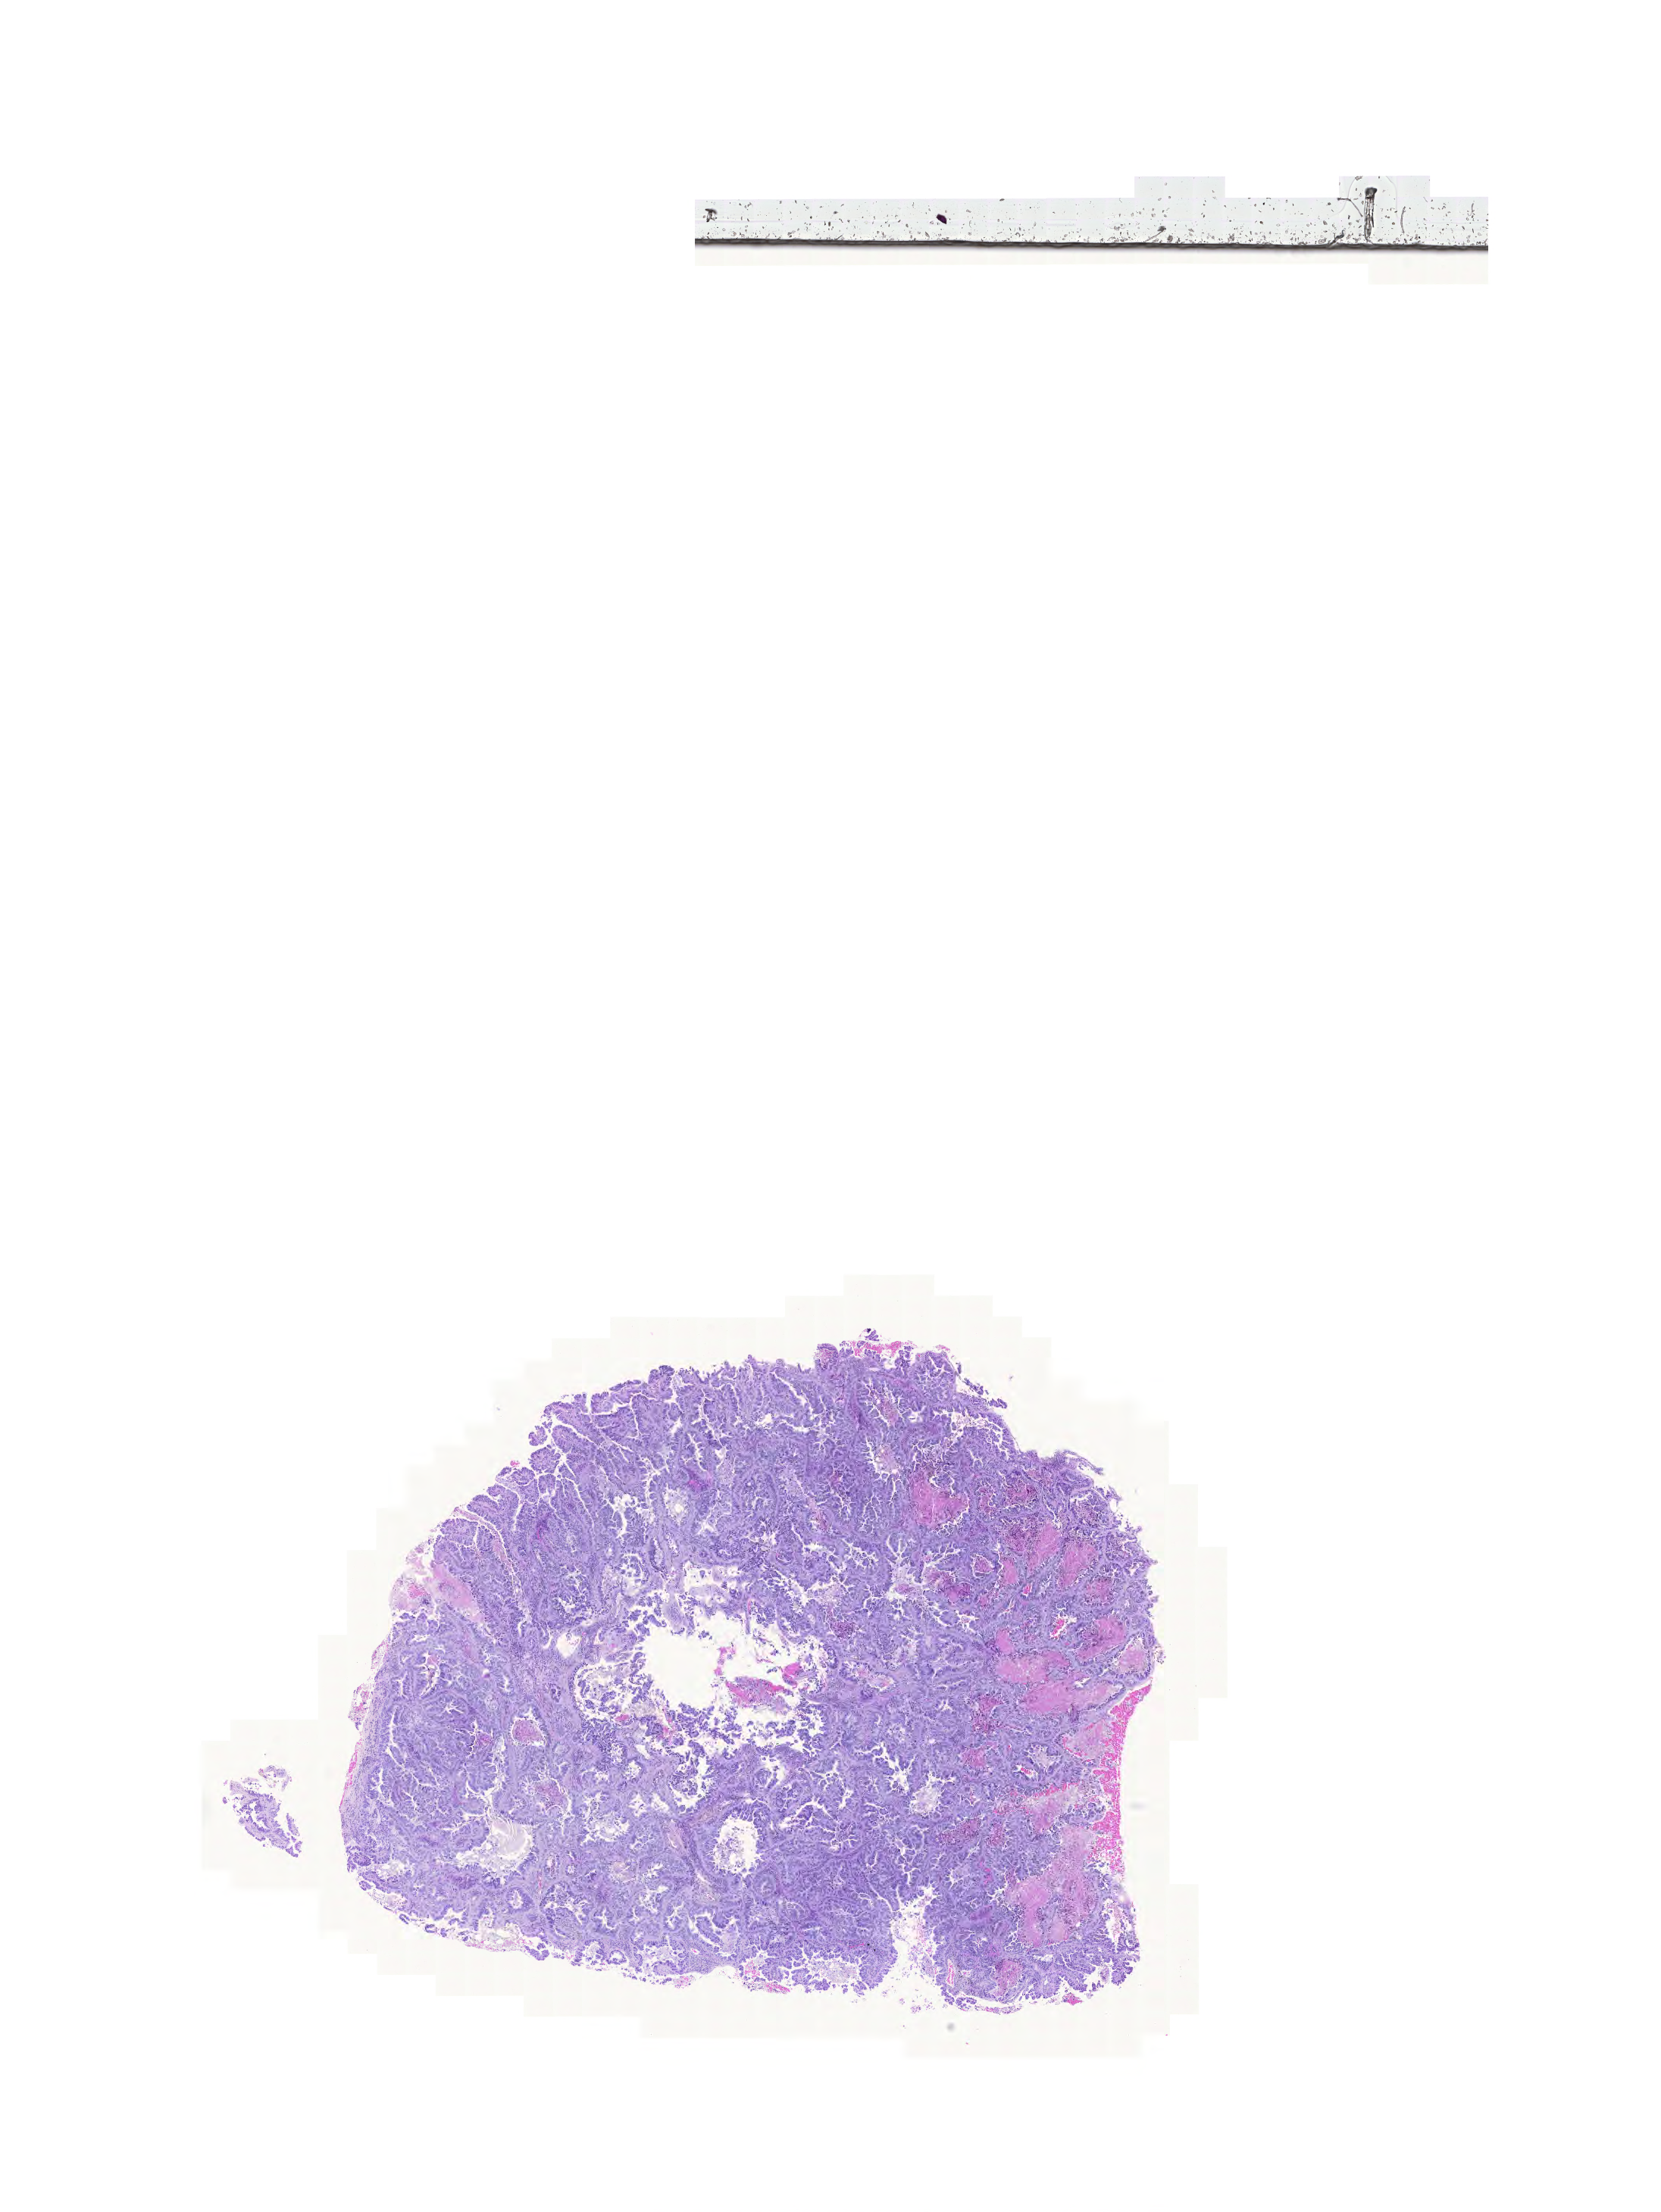
Digitized Hematoxylin and eosin (H&E) stained tissue section (whole slide), low-resolution overview of the scanned area, about 16.3 x 21.7 mm (slide scanned at 20x), formalin-fixed paraffin-embedded (FFPE) diagnostic section, sample: primary tumour, lung. Patient: male, age at initial diagnosis 70 years.
TNM: T3 N0 M0. AJCC pathologic stage: IIB (6th edition). Histologic diagnosis: Adenocarcinoma with mixed subtypes (upper lobe, lung).